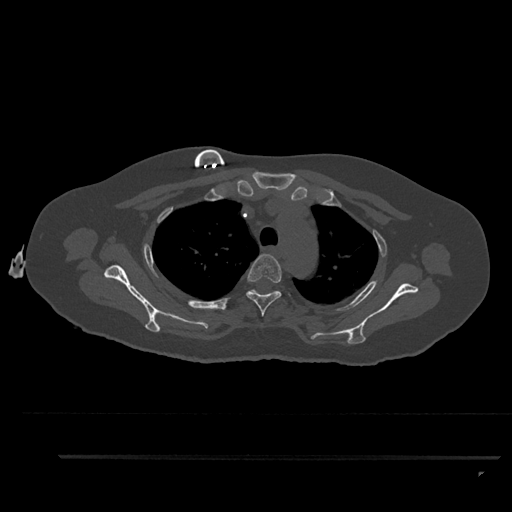
CT including the spine, one axial slice; slice 678 of 797 in the series (ordered by position); reconstruction kernel Br40s/3; 120 kVp; bone window (W 1800 / L 400 HU); 512 × 512 image matrix, field of view 408 × 408 mm. Patient: female, 44 years. Case-level facts recorded for this patient, not image findings: primary cancer: renal; vertebrae with lytic lesions (as recorded): L1.
Outlined on this slice (semi-automatic segmentation, software-assisted and operator-edited):
- T3 vertebra: bounding box (x1, y1, x2, y2) in pixels: (246, 254, 282, 317)
- T4 vertebra: (247, 289, 274, 293)